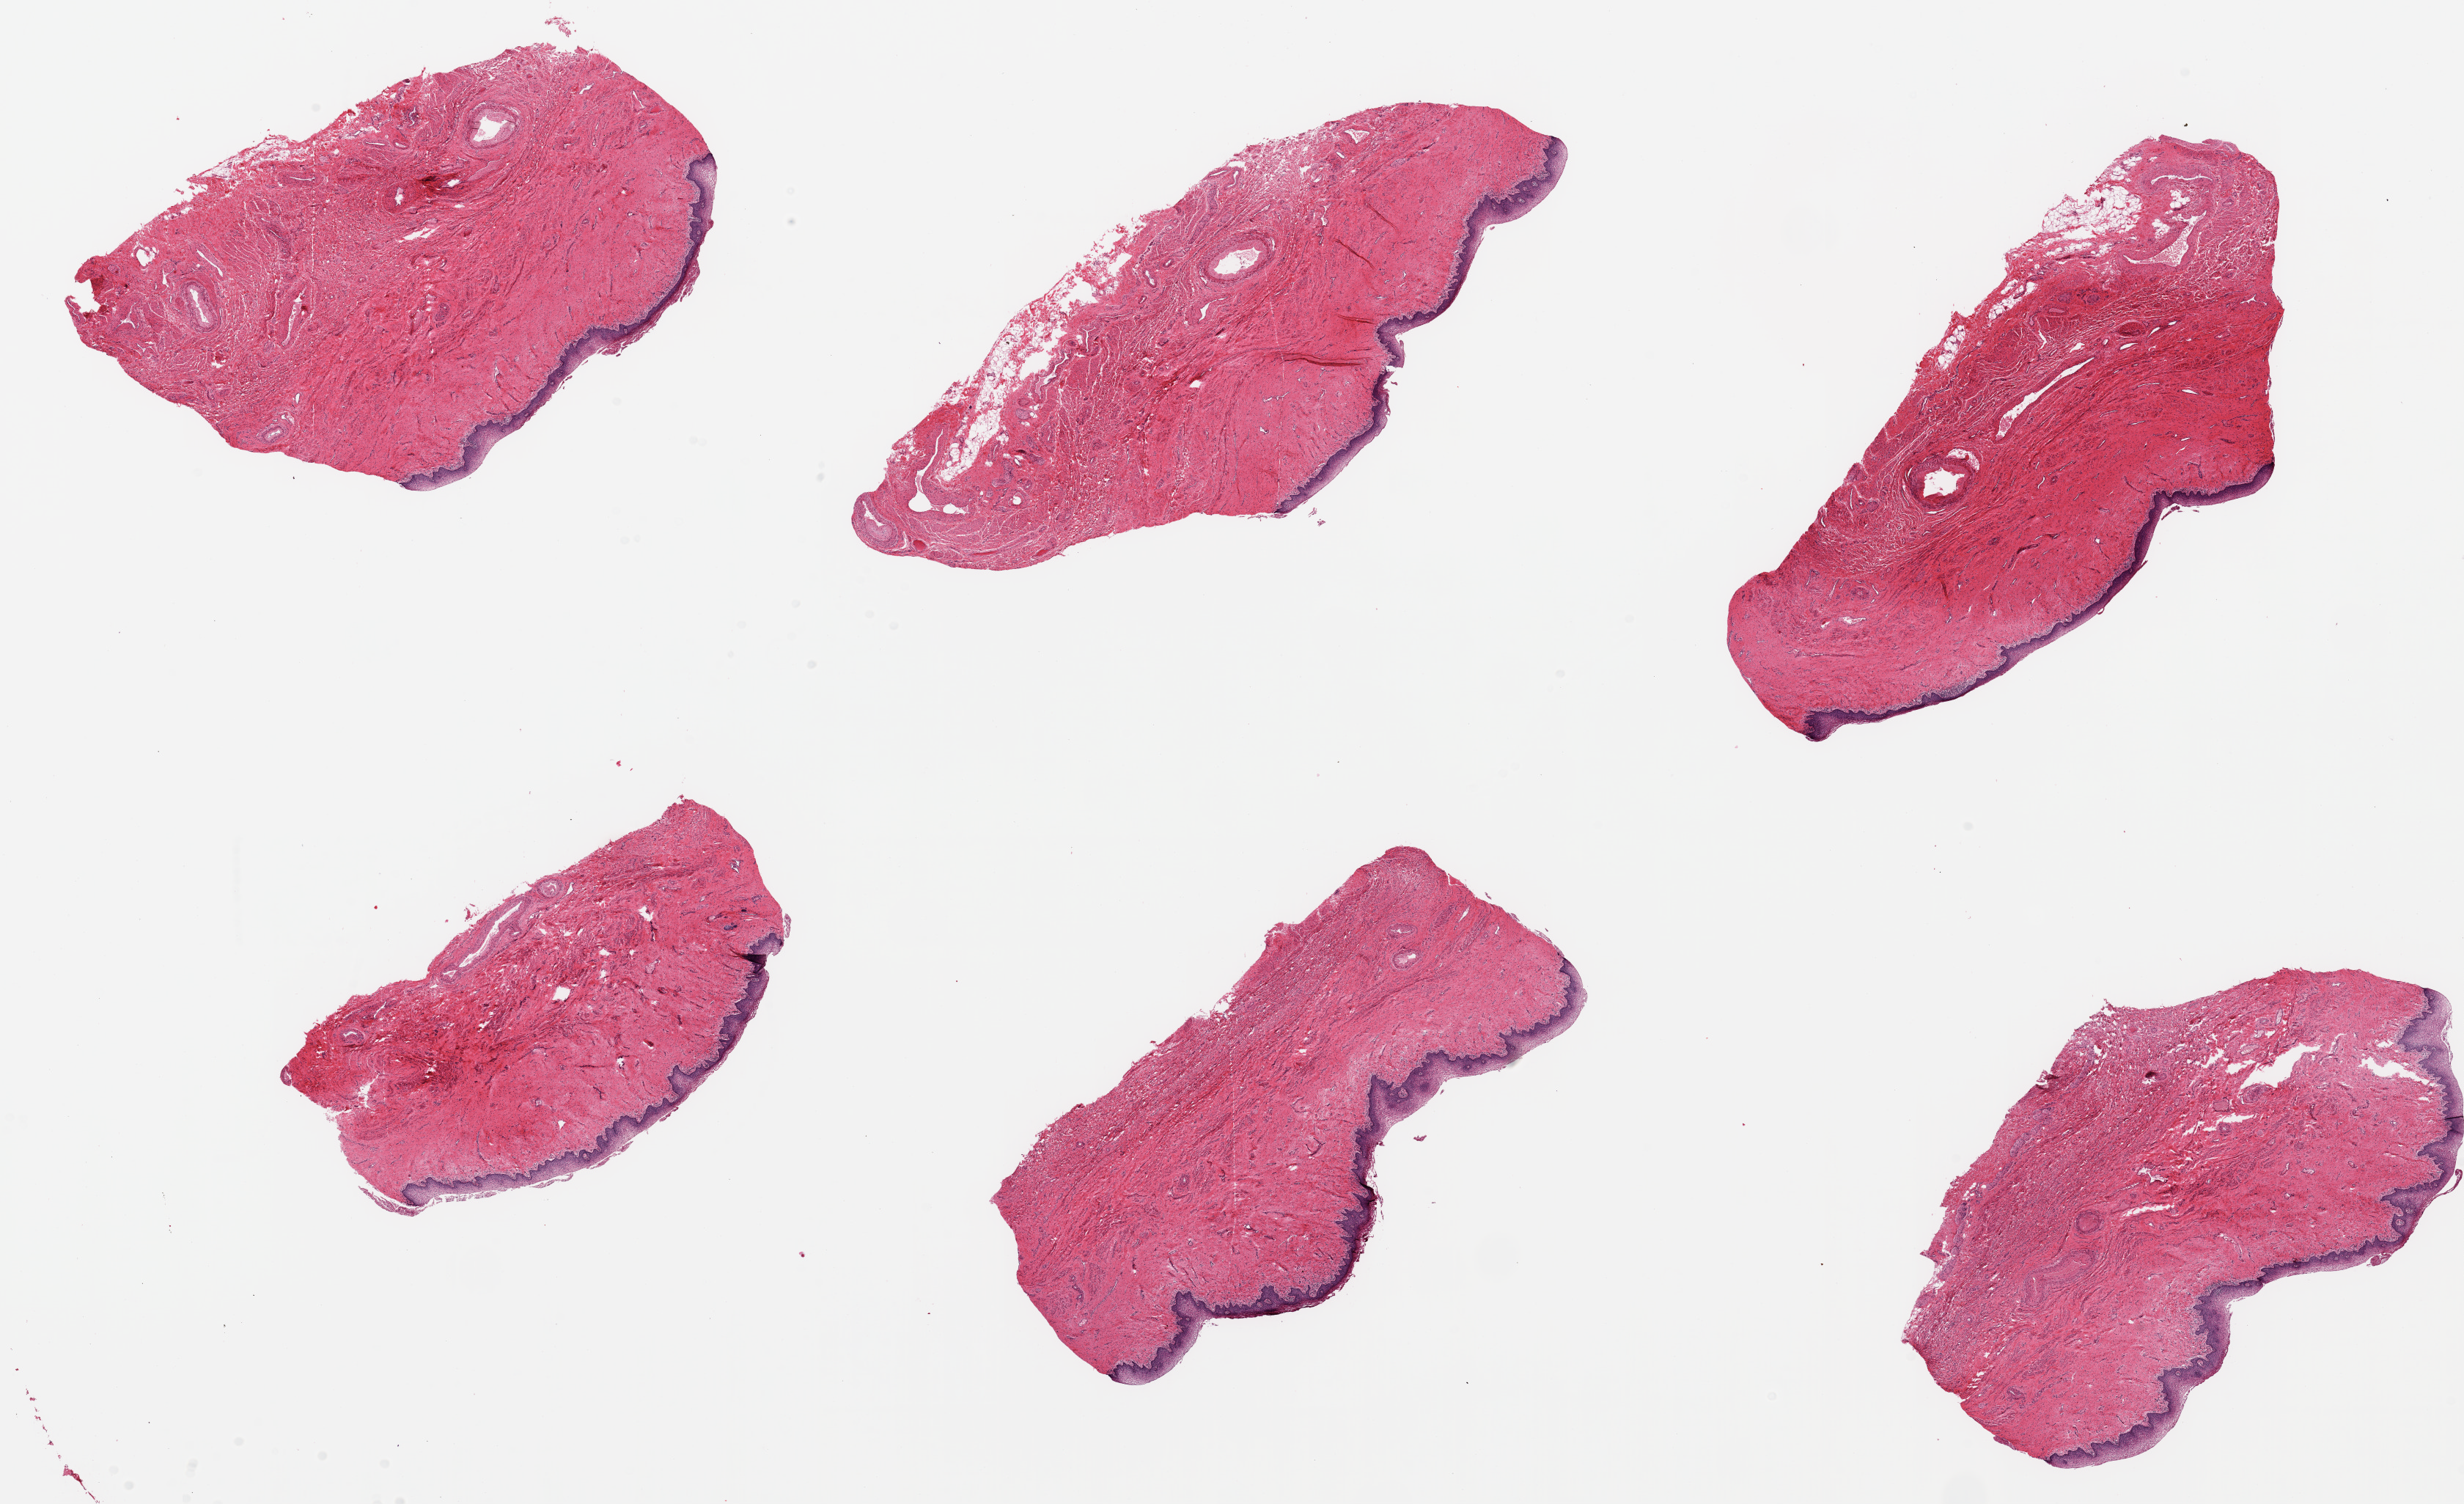
Haematoxylin and eosin whole-slide image — a low-resolution overview of the entire scanned area, about 26.6 x 16.2 mm. PAXgene-fixed, paraffin-embedded tissue. Section of vagina (target tissue). Tissue donor sample. Donor: female.
* review note (as recorded): 6 pieces; mild focal chronic inflammation; partial superficial sloughing of epithelium